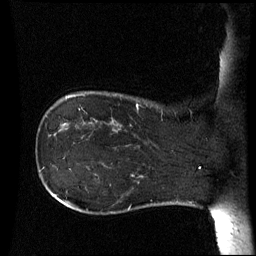
Breast MRI (dynamic contrast-enhanced), one sagittal slice; position 11 of 60 along the scan axis; dynamic contrast-enhanced series, image 2 of 3 at this slice position (ordered by acquisition); 1.5 T; TE 4.2 ms, TR 8.9 ms; 256 × 256 image matrix, field of view 230 × 230 mm. Female patient, age 42 years. From the clinical record (not read from this slice): setting: breast cancer imaged before/during neoadjuvant chemotherapy; receptor status: HER2-positive.
Outlined on this slice (semi-automatic segmentation, software-assisted and operator-edited):
- analysis volume of interest (the breast-tissue region the enhancement analysis was run in; not a lesion): bounding box <106,102,173,150> (left, top, right, bottom; pixels)
- tumour enhancement mask (voxels above the 70 % enhancement threshold inside the analysis volume of interest): <136,103,139,112>